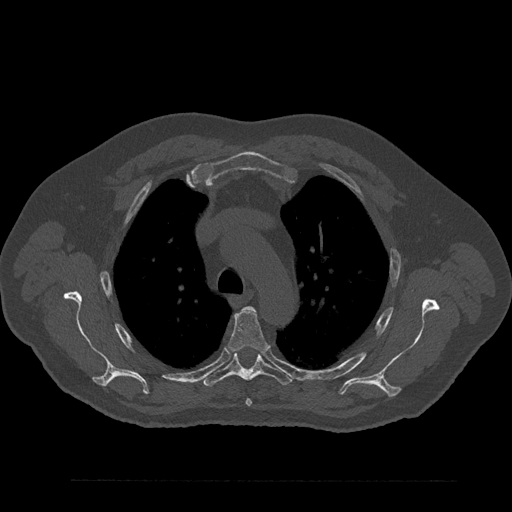
CT including the spine, one axial slice; position 624 of 797 along the scan axis; reconstruction kernel Br40s/3; 120 kVp; bone window (W 1800 / L 400 HU); 0.5 mm slice thickness; 512 × 512 image matrix, field of view 430 × 430 mm. Patient: male, 61 years. Case-level facts recorded for this patient, not image findings: primary cancer: prostate.
Outlined on this slice (semi-automatically segmented with operator editing):
- T4 vertebra: bounding box <228,307,268,406> (left, top, right, bottom; pixels)
- T5 vertebra: <202,352,292,387>